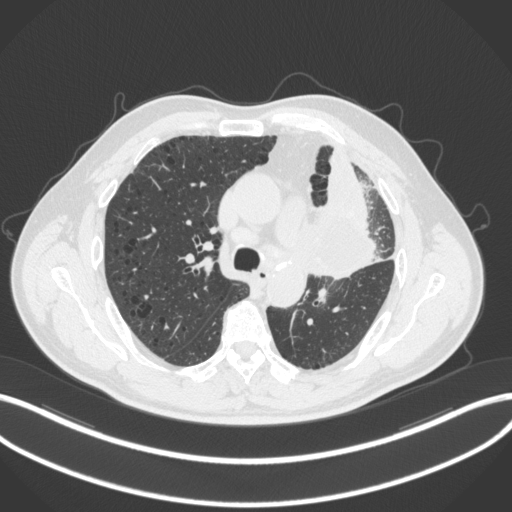
Chest CT, one axial slice; slice 192 of 286 in the series (ordered by position); reconstruction kernel B31f; lung window (W 1500 / L -600 HU); 1 mm slice thickness; 512 × 512 image matrix, field of view 400 × 400 mm. Male patient, age 68 years. From the clinical record (not read from this slice): clinical TNM (as recorded): T3 N3 M1.
Annotated regions visible in this slice (bounding box drawn by a radiologist):
- lung tumour (recorded histology: adenocarcinoma): box from (x=303, y=197) to (x=383, y=284) px